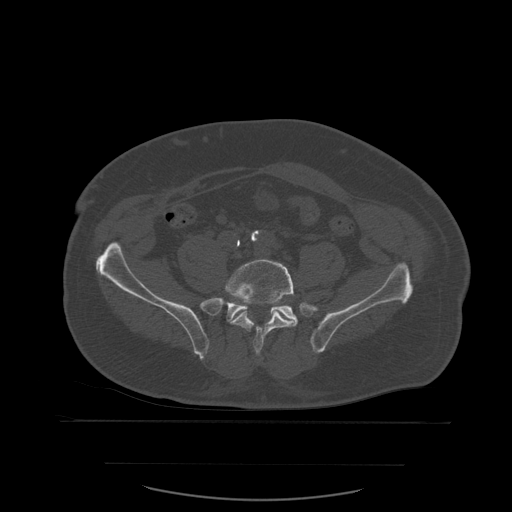
CT including the spine, one axial slice; slice 131 of 590 in the series (ordered by position); bone window (W 1800 / L 400 HU); 1.25 mm slice thickness; 512 × 512 image matrix, field of view 479 × 479 mm. Patient age 71 years. Case-level facts recorded for this patient, not image findings: primary cancer: lung.
Structures marked on this image (semi-automatically segmented with operator editing):
- L5 vertebra: box from (x=225, y=260) to (x=297, y=357) px